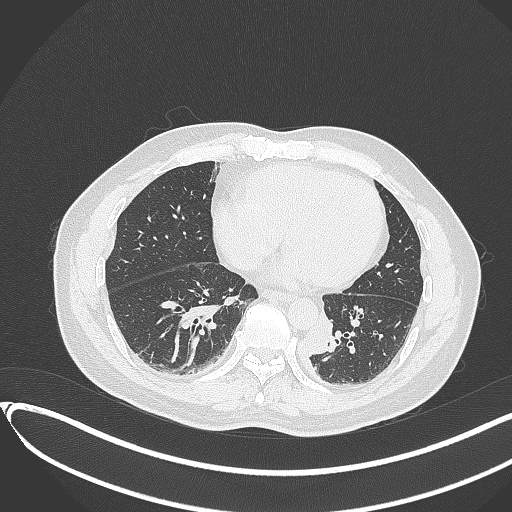
Chest CT, one axial slice. Position 117 of 417 along the scan axis. 120 kVp. Lung window (W 1500 / L -600 HU). 512 × 512 image matrix, field of view 400 × 400 mm. Male patient, age 54 years. From the clinical record (not read from this slice): clinical TNM (as recorded): T3 N0 M0.
Outlined on this slice (rectangle marked by the reading radiologist):
- lung tumour (recorded histology: squamous cell carcinoma): box from (x=301, y=314) to (x=337, y=366) px